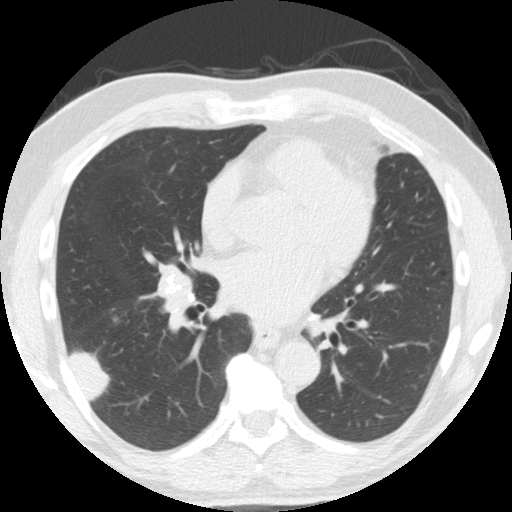
Low-dose screening chest CT, axial slice. Second screening round (one year after baseline). Lung window (W 1500 / L -600 HU). 2.5 mm slice thickness. Standard (soft-tissue) reconstruction kernel (STANDARD). 120 kVp. Slice 94 of 174 in the series. 512 × 512 image matrix, field of view 341 × 341 mm. Male, age 61 years at enrolment.
Lesion marked by an expert reader, box from (x=50, y=326) to (x=117, y=401) px. The exam's reader record, not a measurement of the box and not confirmed to be the same lesion: non-calcified nodule or mass ≥4 mm, right lower lobe, 33 × 19 mm, smooth margins, soft tissue attenuation, pre-existing on the prior screen: yes; interval growth: yes.